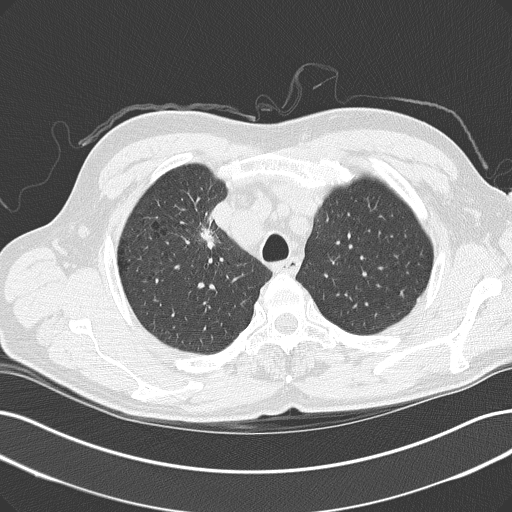
Chest CT (low-dose screening protocol), one axial image; baseline screening round; lung window (W 1500 / L -600 HU); 2 mm slice thickness; 120 kVp; slice 34 of 152 in the series. Male, age 61 years at enrolment. Current smoker at enrolment.
Expert reader's lesion annotation, box from (x=188, y=218) to (x=246, y=266) px. The screening reader recorded 2 non-calcified nodules or masses ≥4 mm on this exam; which of them this box marks is not recorded. Official screen result: positive, change unspecified: nodule(s) >= 4 mm or enlarging nodule(s), mass(es), or other non-specific abnormalities suspicious for lung cancer.